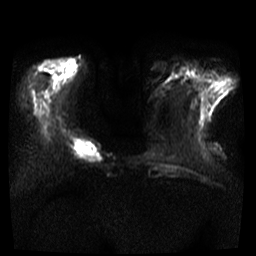
Breast MRI, one axial slice. Position 9 of 35 along the scan axis. Diffusion-weighted series; image 2 of 4 stored at this slice position (different b-values; order by instance number). 3 T. 5 mm slice thickness. 256 × 256 image matrix, field of view 300 × 300 mm. Female patient.
Outlined on this slice (manually delineated by an expert):
- tumour on diffusion-weighted imaging: bounding box (x1, y1, x2, y2) in pixels: (73, 139, 102, 163)